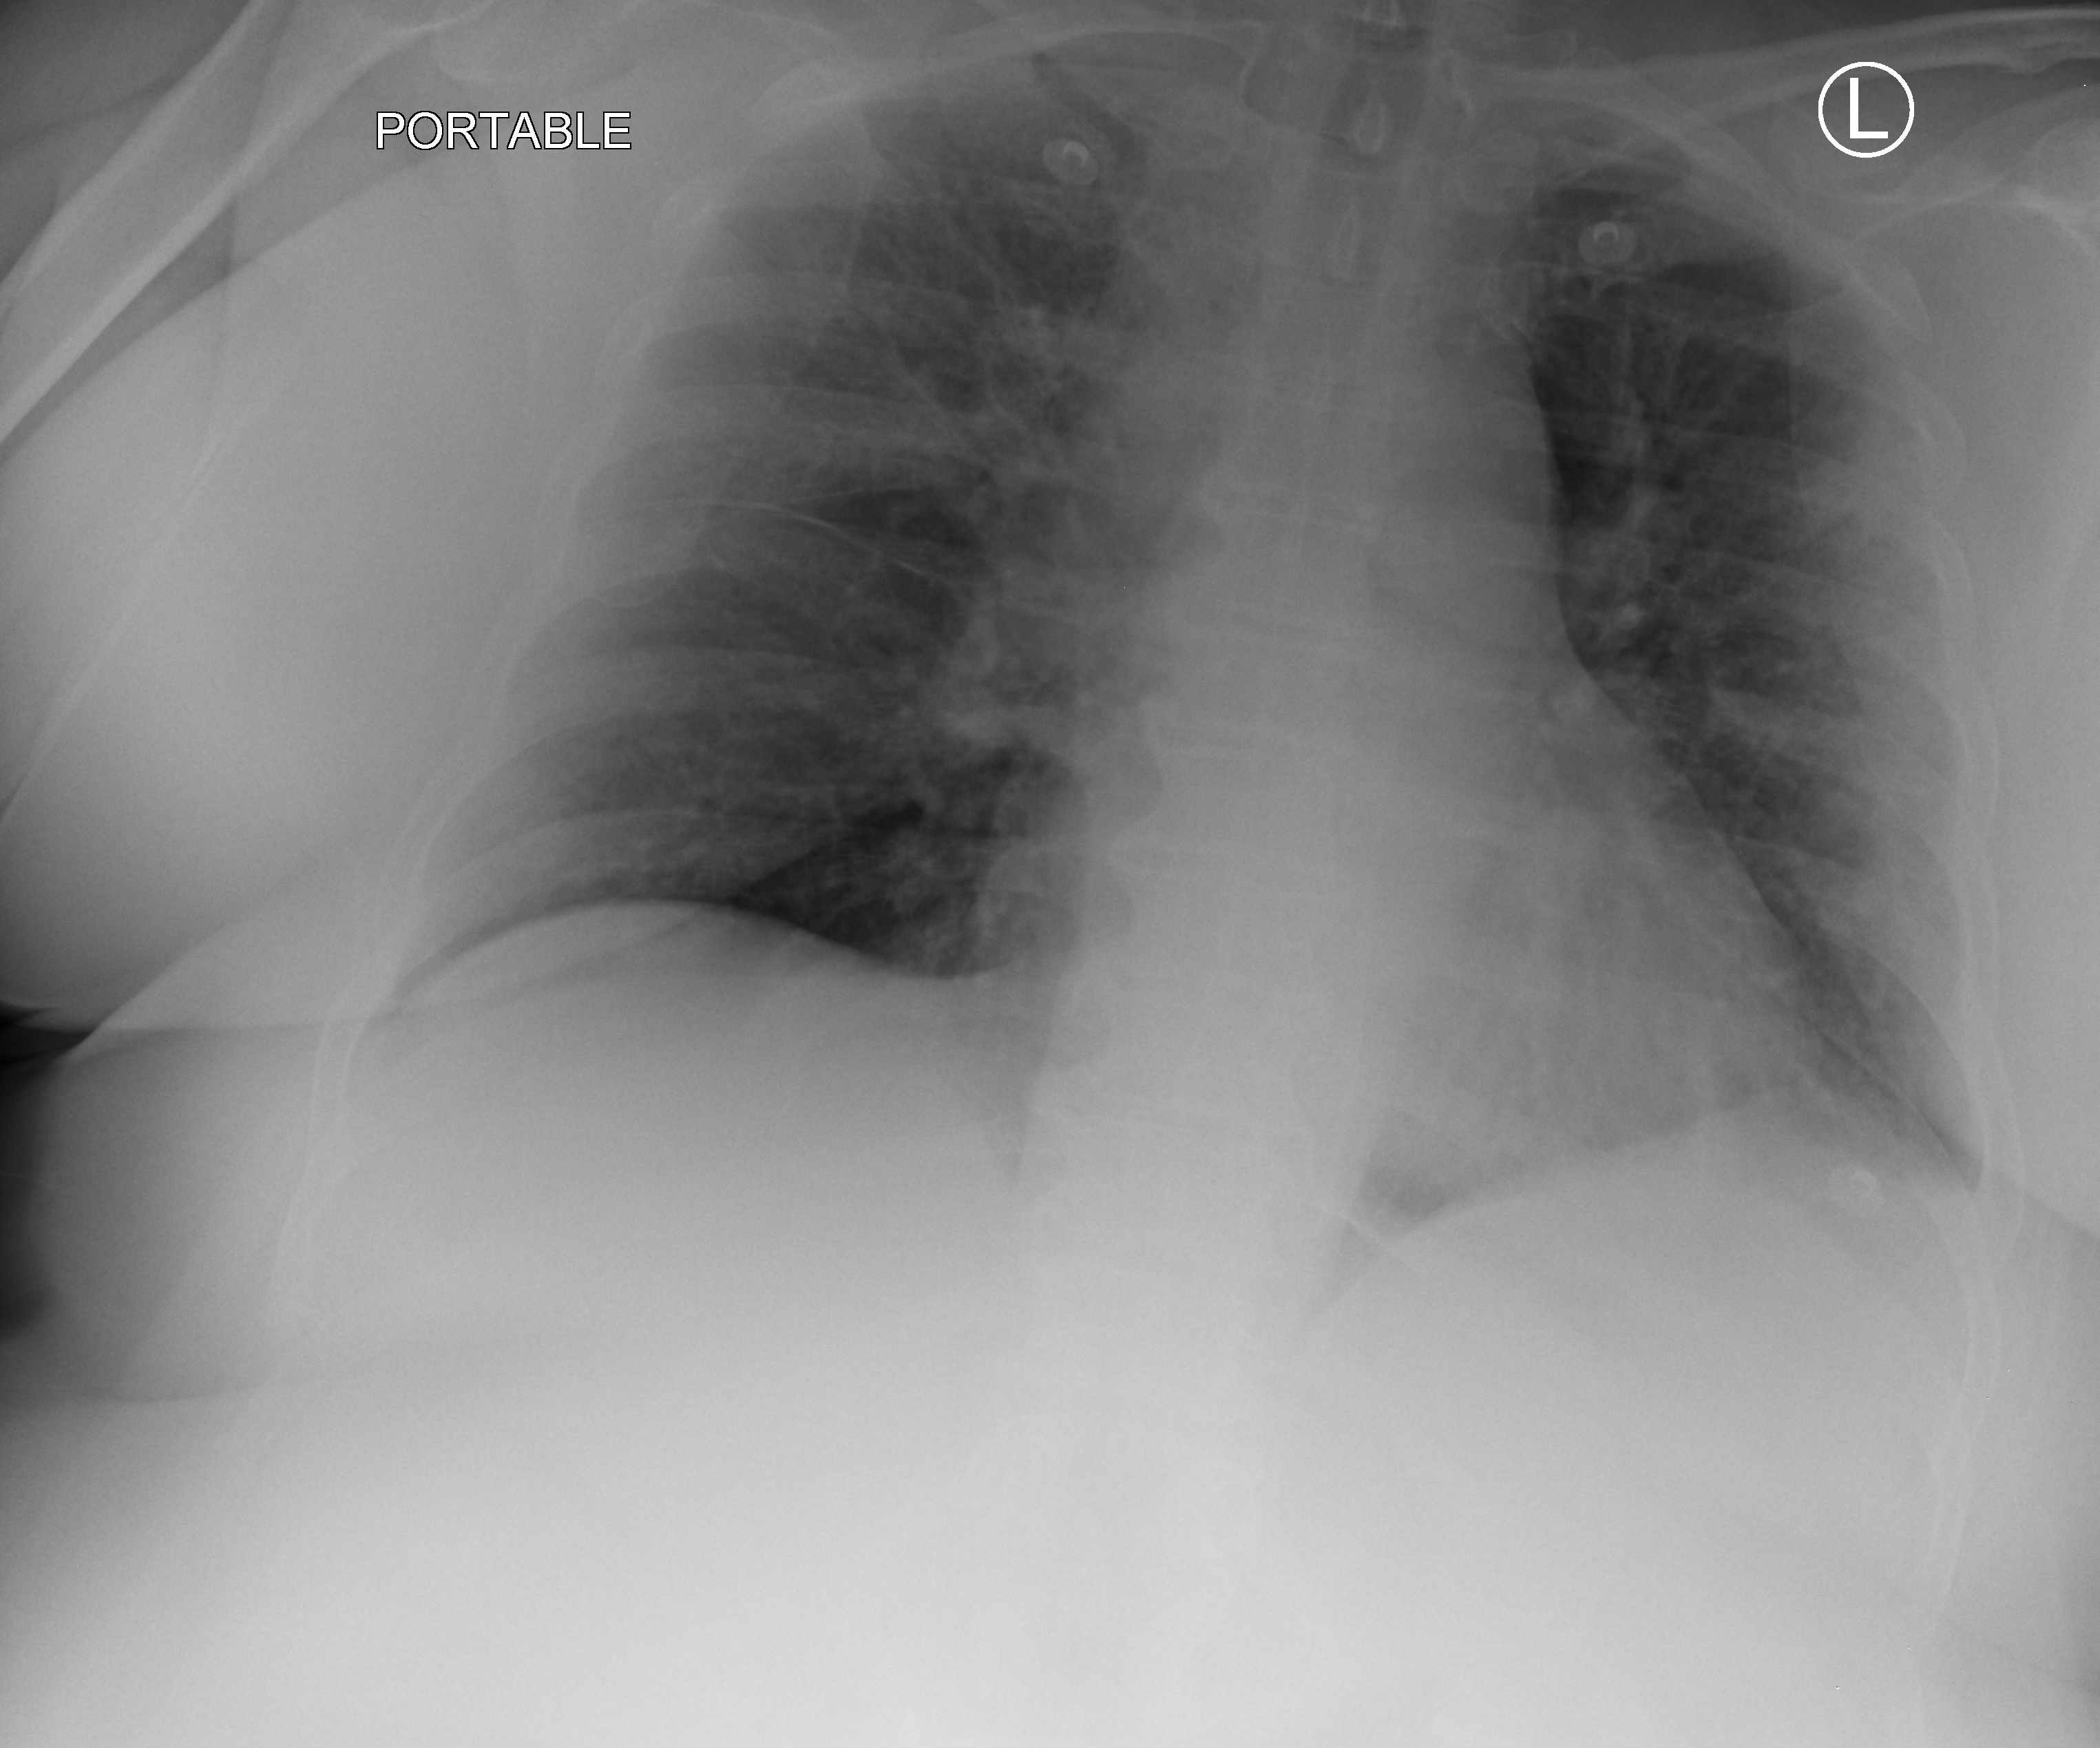
Portable chest radiograph, anteroposterior (AP) projection. Female patient hospitalised with COVID-19, age 60–74 years.
Admission-level facts for this patient (not findings on this image; timing relative to this image not recorded): admitted to intensive care during this hospital stay: no.